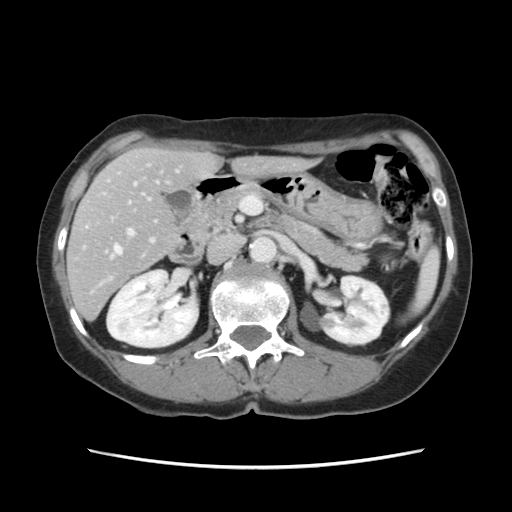
Contrast-enhanced abdominal CT, one axial slice. Slice 60 of 120 in the series (ordered by position). Soft-tissue window (W 400 / L 40 HU). 512 × 512 image matrix, field of view 330 × 330 mm. Female patient, age 70 years. Case-level facts recorded for this patient, not image findings: diagnosis: colorectal cancer liver metastases, imaged before liver resection; multiple liver metastases: no; largest metastasis: 2.5 cm; disease in both lobes: no.
Annotated regions visible in this slice (manually delineated by an expert):
- hepatic veins: bounding box [x1, y1, x2, y2] px = [114, 246, 121, 255]
- liver: [69, 148, 301, 319]
- planned liver remnant (the part of the liver to remain after resection): [68, 148, 301, 289]
- portal vein (with intrahepatic branches): [127, 170, 178, 242]